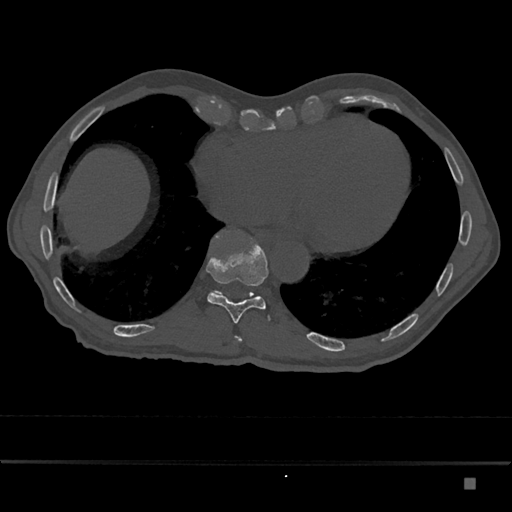
CT including the spine, one axial slice. Position 734 of 797 along the scan axis. 120 kVp. Bone window (W 1800 / L 400 HU). 0.5 mm slice thickness. 512 × 512 image matrix, field of view 390 × 390 mm. Patient: male, 72 years. From the clinical record (not read from this slice): primary cancer: prostate.
Structures marked on this image (semi-automatically segmented with operator editing):
- T10 vertebra: bounding box [x1, y1, x2, y2] px = [206, 235, 269, 323]
- T11 vertebra: [208, 236, 254, 296]
- T9 vertebra: [236, 337, 242, 342]